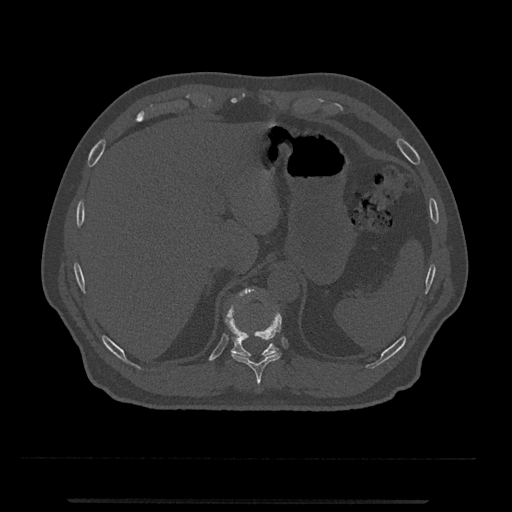
CT including the spine, one axial slice; slice 495 of 797 in the series (ordered by position); reconstruction kernel Br40s/3; bone window (W 1800 / L 400 HU); 0.5 mm slice thickness; 512 × 512 image matrix. Patient: male, 63 years. Case-level facts recorded for this patient, not image findings: primary cancer: prostate.
Outlined on this slice (semi-automatic segmentation, software-assisted and operator-edited):
- T10 vertebra: box from (x=231, y=310) to (x=282, y=385) px
- T11 vertebra: (x=225, y=288)–(x=279, y=356)